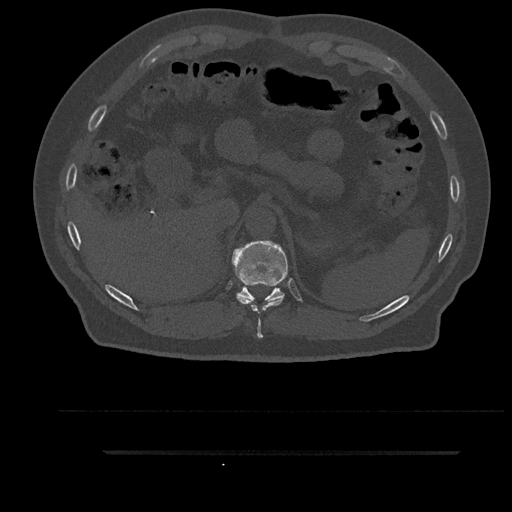
CT including the spine, one axial slice; position 333 of 797 along the scan axis; 120 kVp; bone window (W 1800 / L 400 HU); 0.5 mm slice thickness; 512 × 512 image matrix, field of view 432 × 432 mm. Patient: male, 63 years. From the clinical record (not read from this slice): primary cancer: renal; vertebrae with lytic lesions (as recorded): T8.
Outlined on this slice (semi-automatically segmented with operator editing):
- T10 vertebra: bounding box <237,297,284,338> (left, top, right, bottom; pixels)
- T11 vertebra: <232,241,288,302>